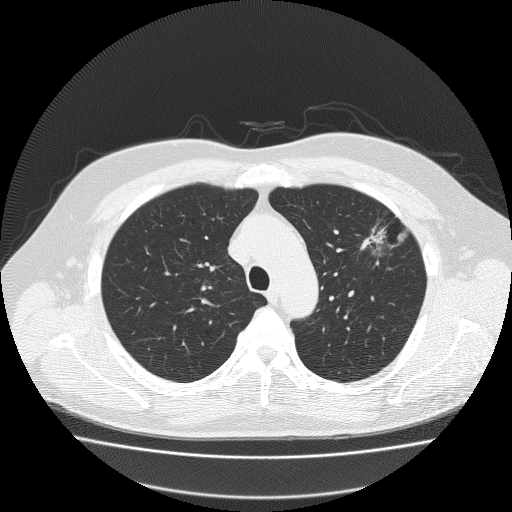
Low-dose screening chest CT, one axial slice. Position 152 of 204 along the scan axis. Reconstruction kernel FC51. 120 kVp. Lung window (W 1500 / L -600 HU). 2 mm slice thickness. 512 × 512 image matrix, field of view 410 × 410 mm.
Outlined on this slice (outlined manually by an expert reader):
- lesion 1 (tumor, upper lobe of left lung): box from (x=361, y=225) to (x=404, y=252) px